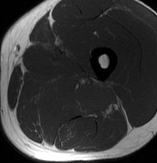
MRI of an extremity soft-tissue mass, one axial slice. MR volume resampled by the dataset authors to the PET/CT grid (not the native acquisition matrix). 3.27 mm slice thickness. 157 × 163 image matrix, field of view 153 × 159 mm. Male patient. Case-level facts recorded for this patient, not image findings: histological type: extraskeletal osteosarcoma; grade: high; site of the primary tumour: left adductur.
Outlined on this slice (expert contour drawn on MRI and transferred to this co-registered scan by the dataset authors):
- gross tumour volume (mass): bounding box [x1, y1, x2, y2] px = [17, 72, 123, 120]